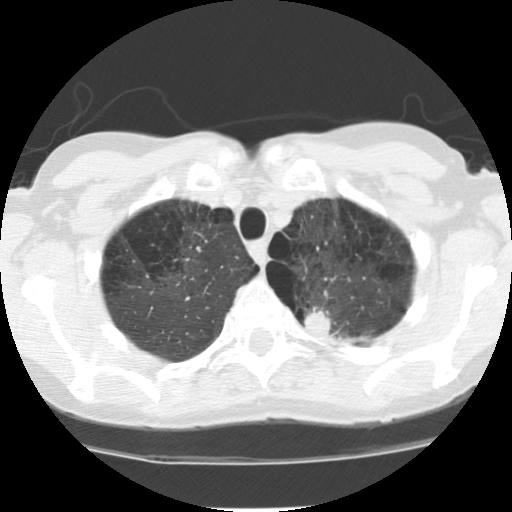
Low-dose screening chest CT, one axial slice. Slice 98 of 116 in the series (ordered by position). Reconstruction kernel STANDARD. 120 kVp. Lung window (W 1500 / L -600 HU). 512 × 512 image matrix.
Structures marked on this image (outlined manually by an expert reader):
- lesion 1 (tumor, upper lobe of left lung): bounding box [x1, y1, x2, y2] px = [304, 308, 339, 338]